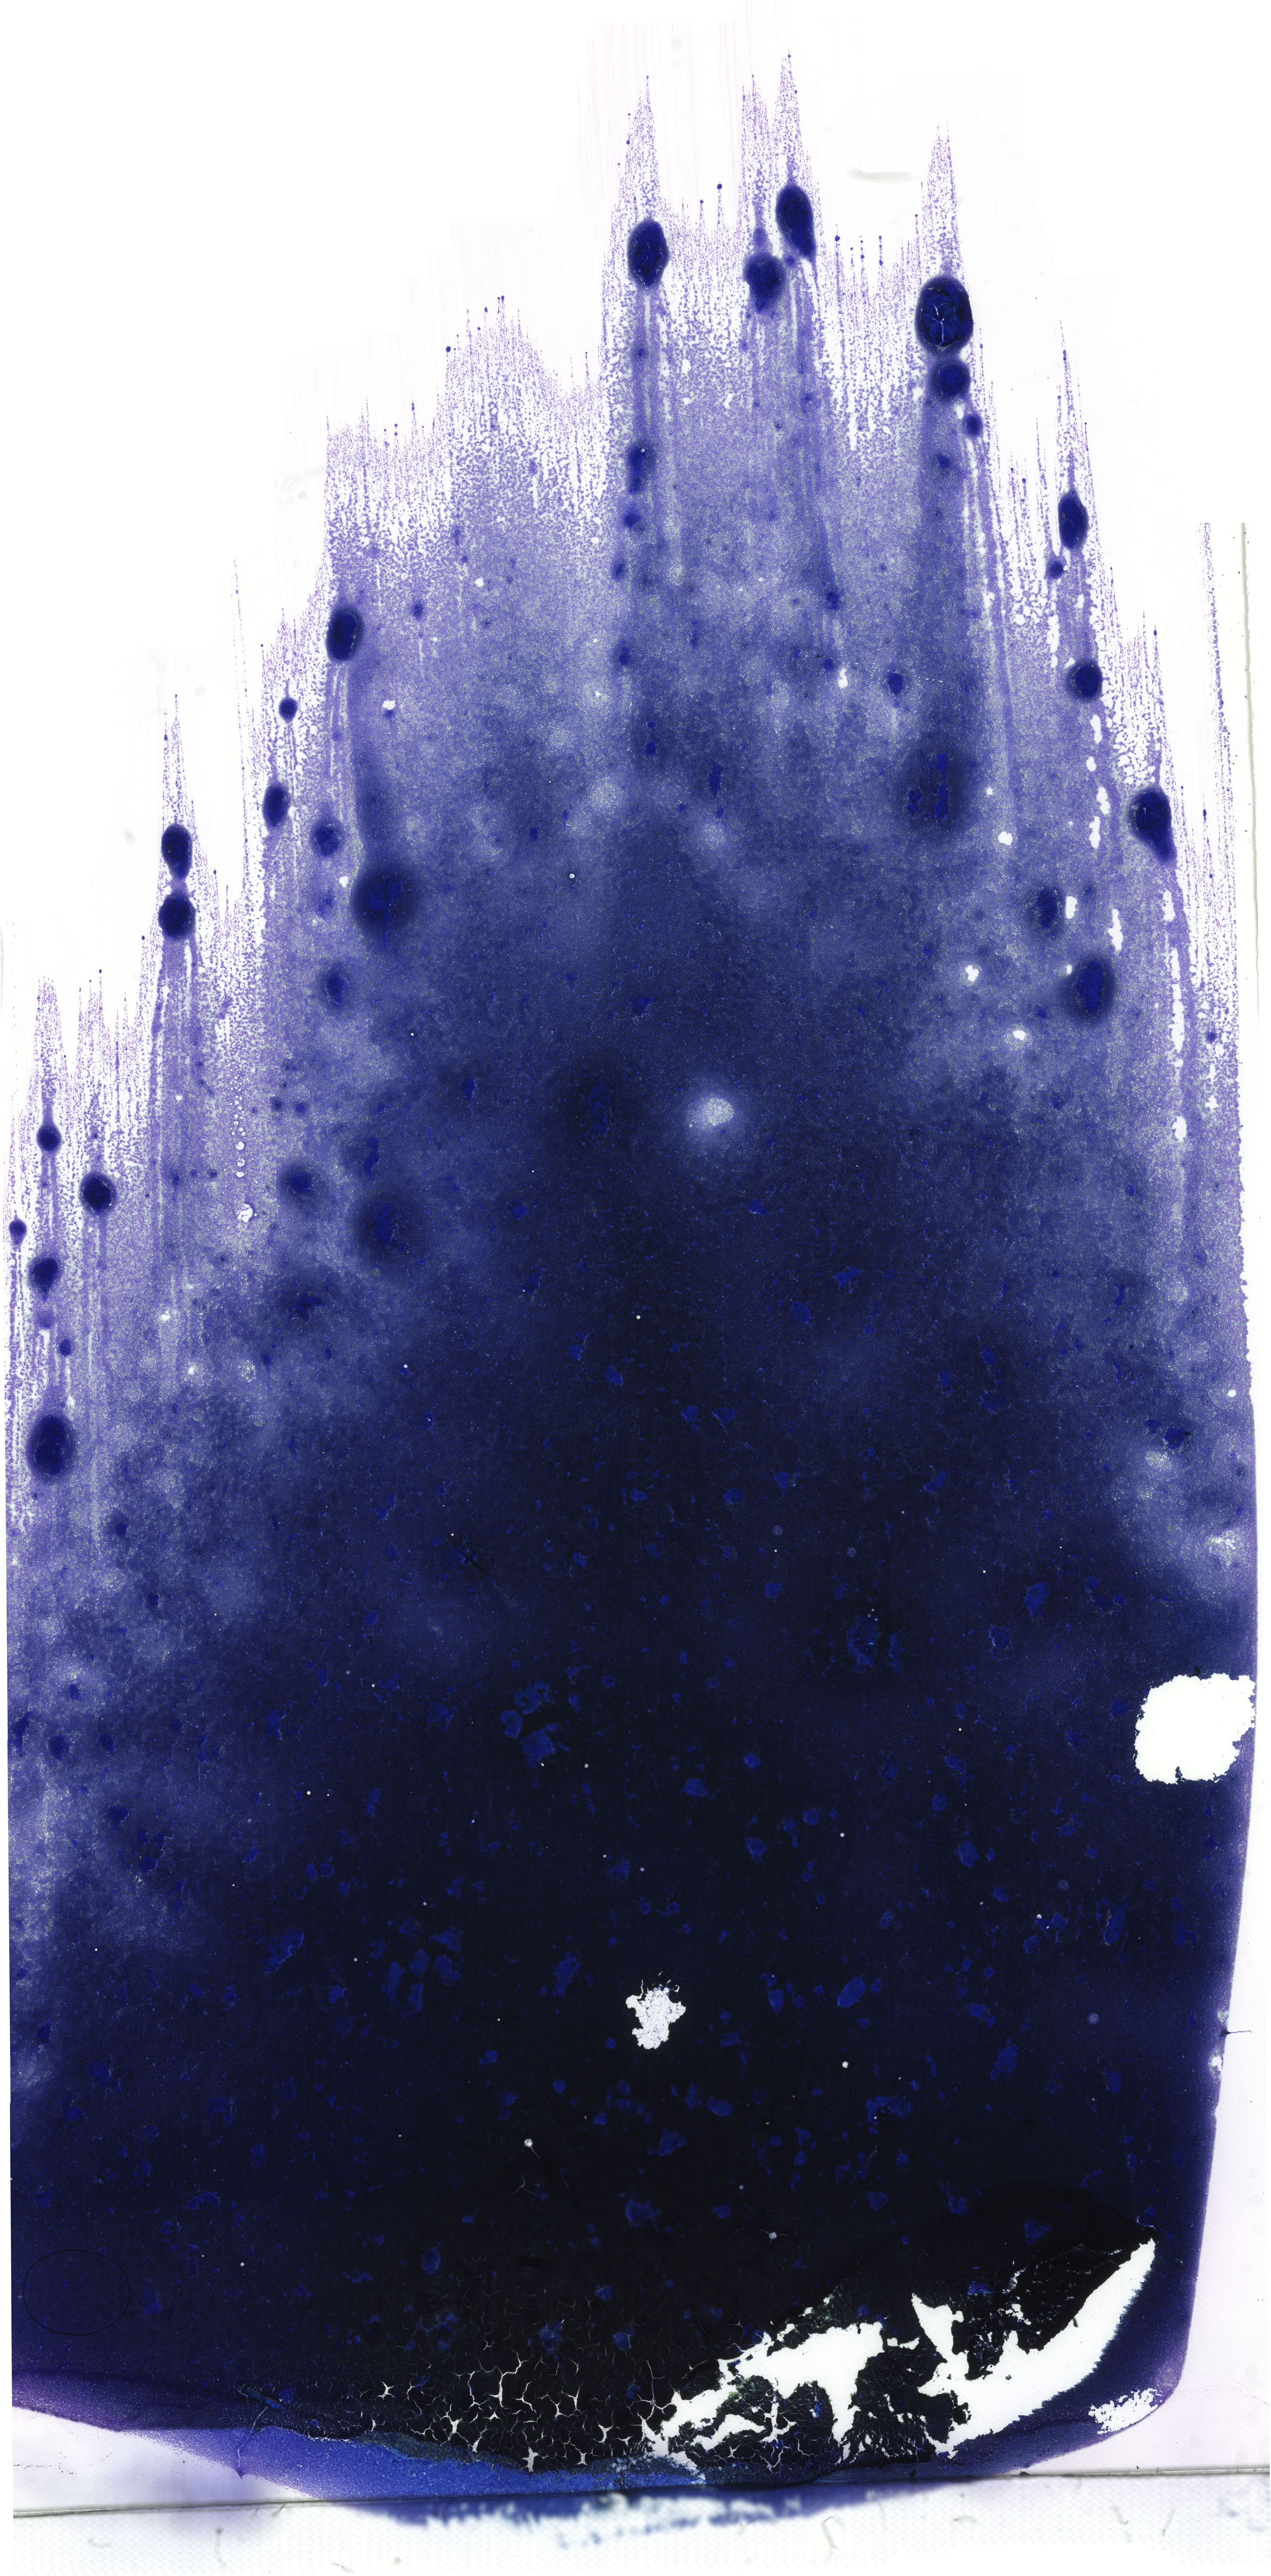
May-Grünwald-Giemsa (MGG)-stained marrow aspirate smear (whole slide) — low-resolution overview of the scanned area, about 20.7 x 42.1 mm. Male patient.
* diagnosis: Chronic Phase Chronic Myeloid Leukemia, BCR-ABL1 Positive